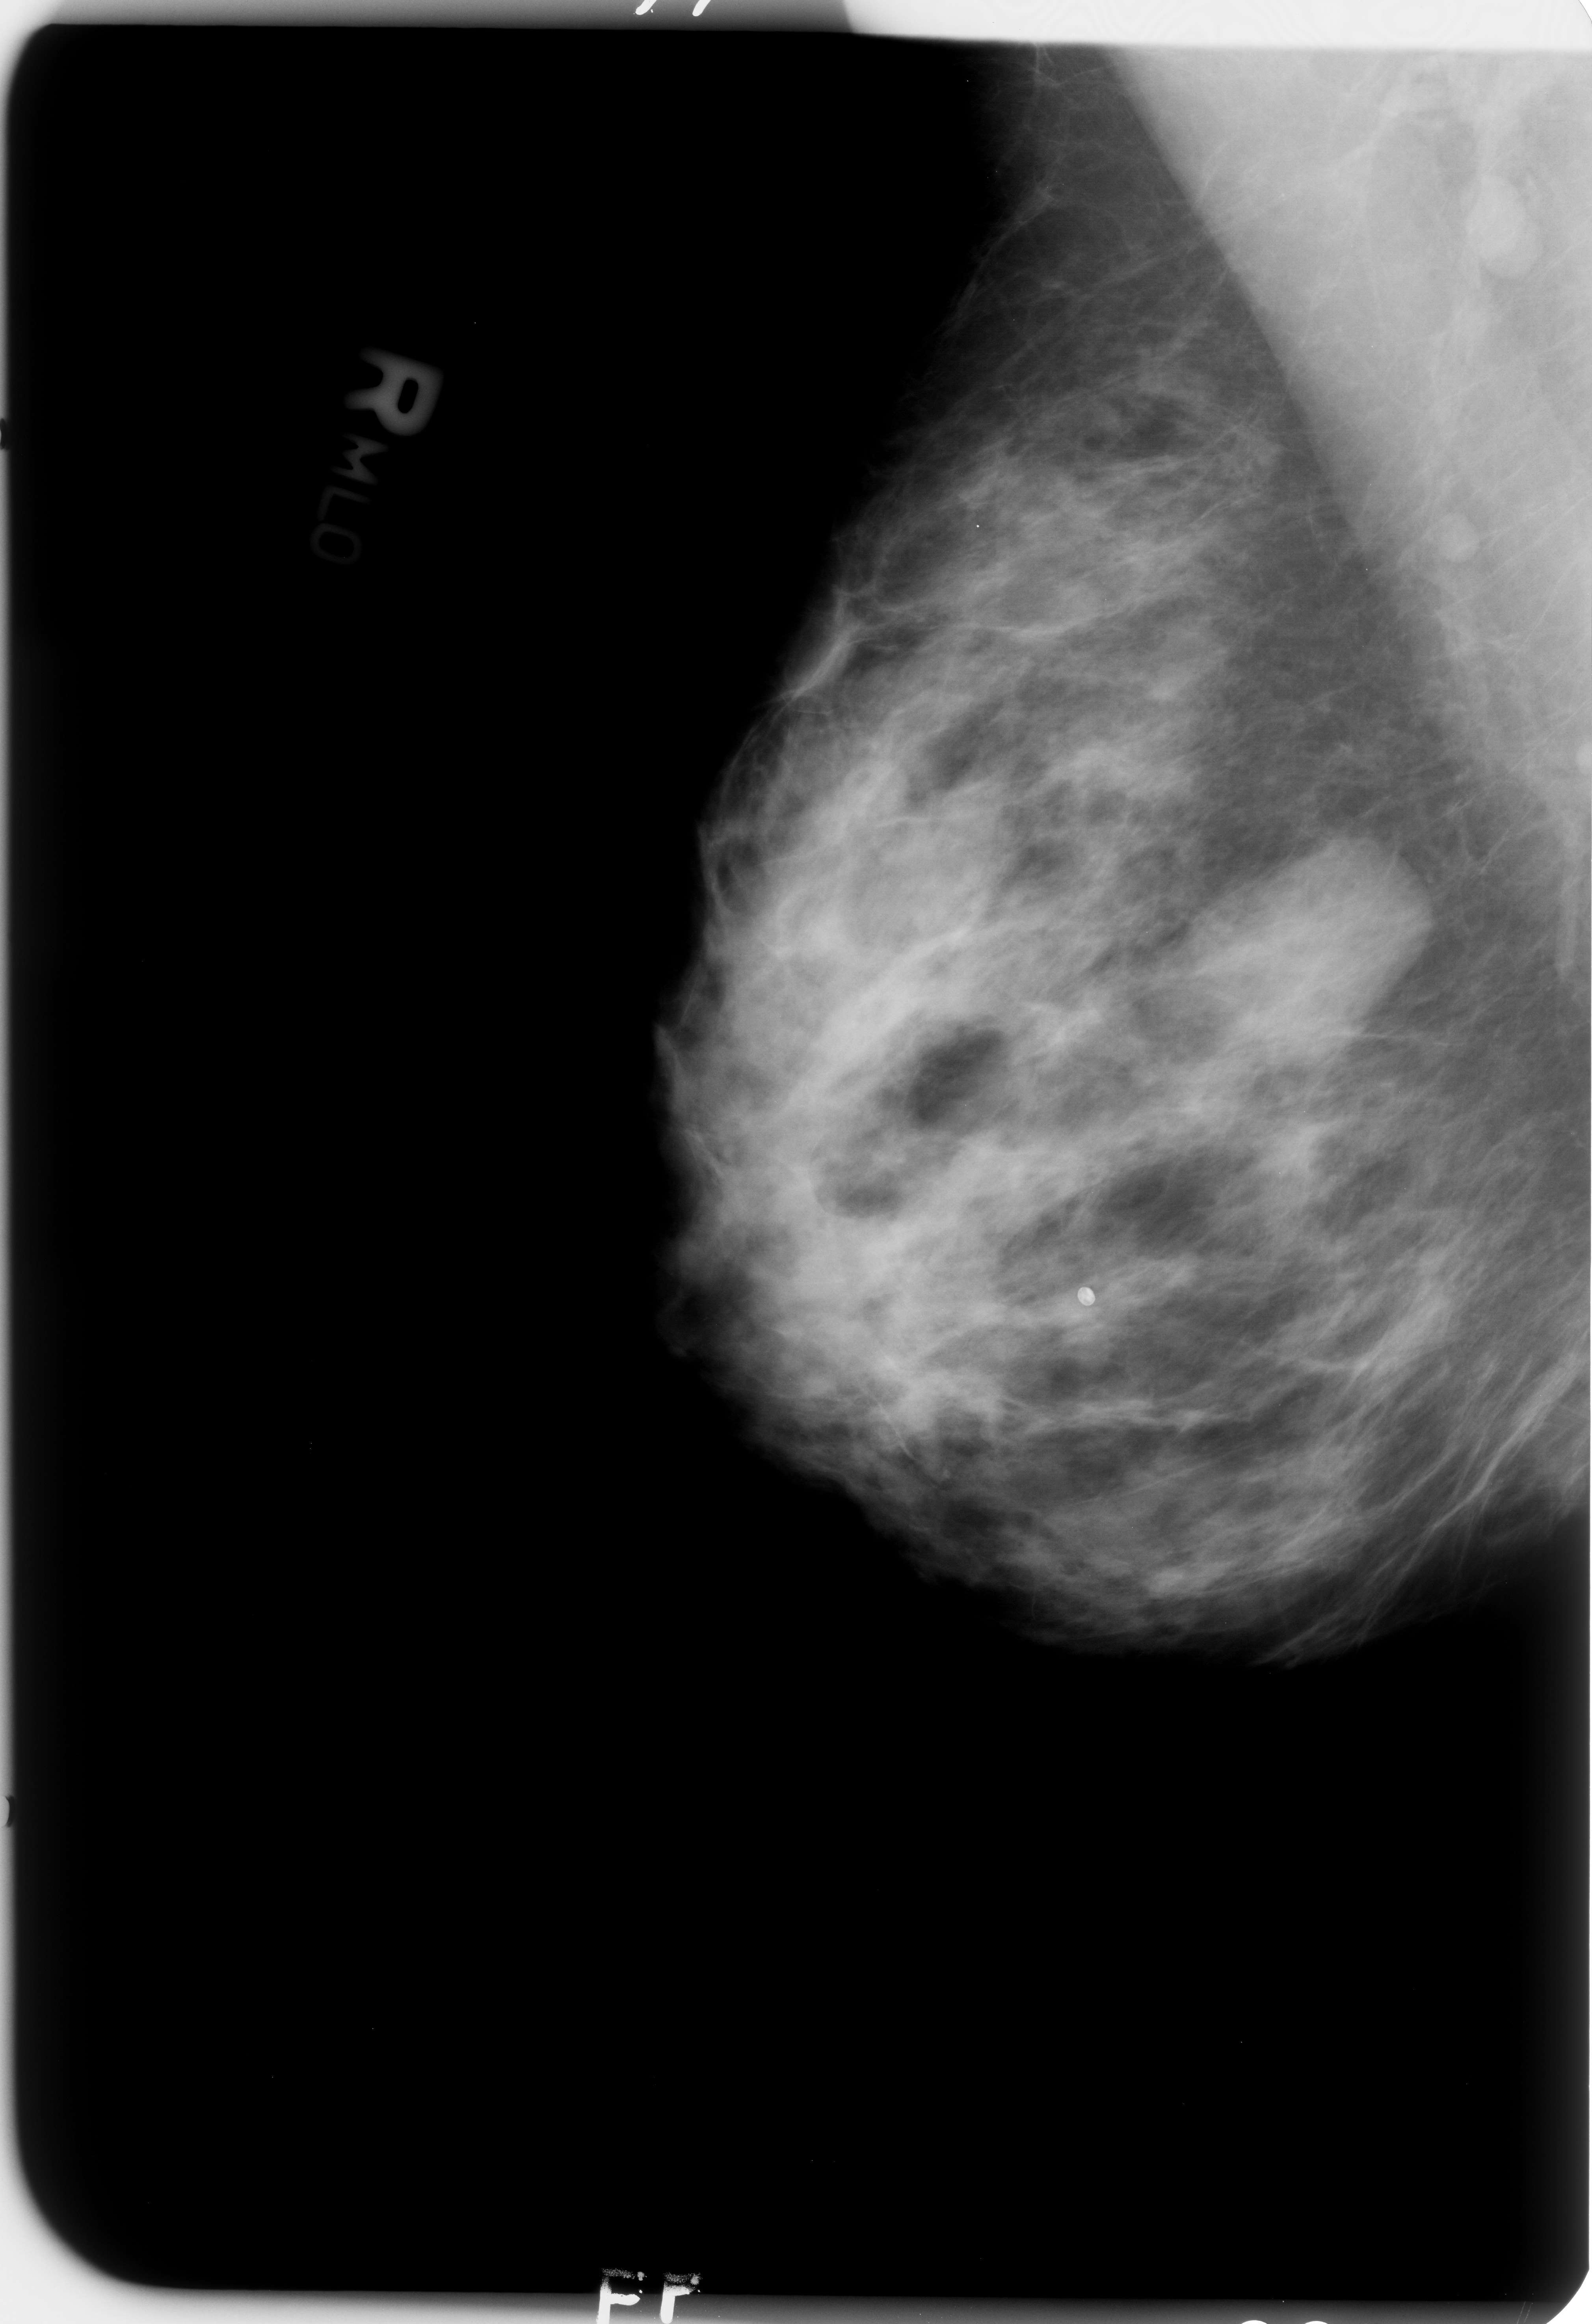
Mammogram (digitized film); right breast; MLO view; breast composition: heterogeneously dense (BI-RADS density category 3 of 4).
Marked abnormality: mass, shape oval, margins circumscribed / obscured; BI-RADS assessment category 3; pathology result (as recorded, not read from the image): benign.